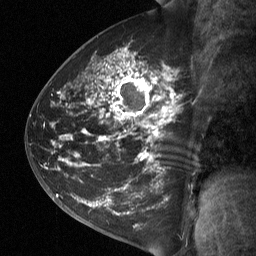
Breast MRI (dynamic contrast-enhanced), one sagittal slice; dynamic contrast-enhanced study with each time point stored as its own series, time point 2 of 3 at this slice position (early post-contrast, ordered by acquisition time); 1.5 T; TE 4.8 ms, TR 27 ms; 2 mm slice thickness; 256 × 256 image matrix, field of view 200 × 200 mm. Patient: female, 42 years. Case-level facts recorded for this patient, not image findings: setting: breast cancer imaged before/during neoadjuvant chemotherapy; receptor status: triple-negative.
Annotated regions visible in this slice (semi-automatic segmentation, software-assisted and operator-edited):
- analysis volume of interest (the breast-tissue region the enhancement analysis was run in; not a lesion): bounding box <49,45,200,197> (left, top, right, bottom; pixels)
- tumour enhancement mask (voxels above the 90 % enhancement threshold inside the analysis volume of interest): <69,53,176,165>